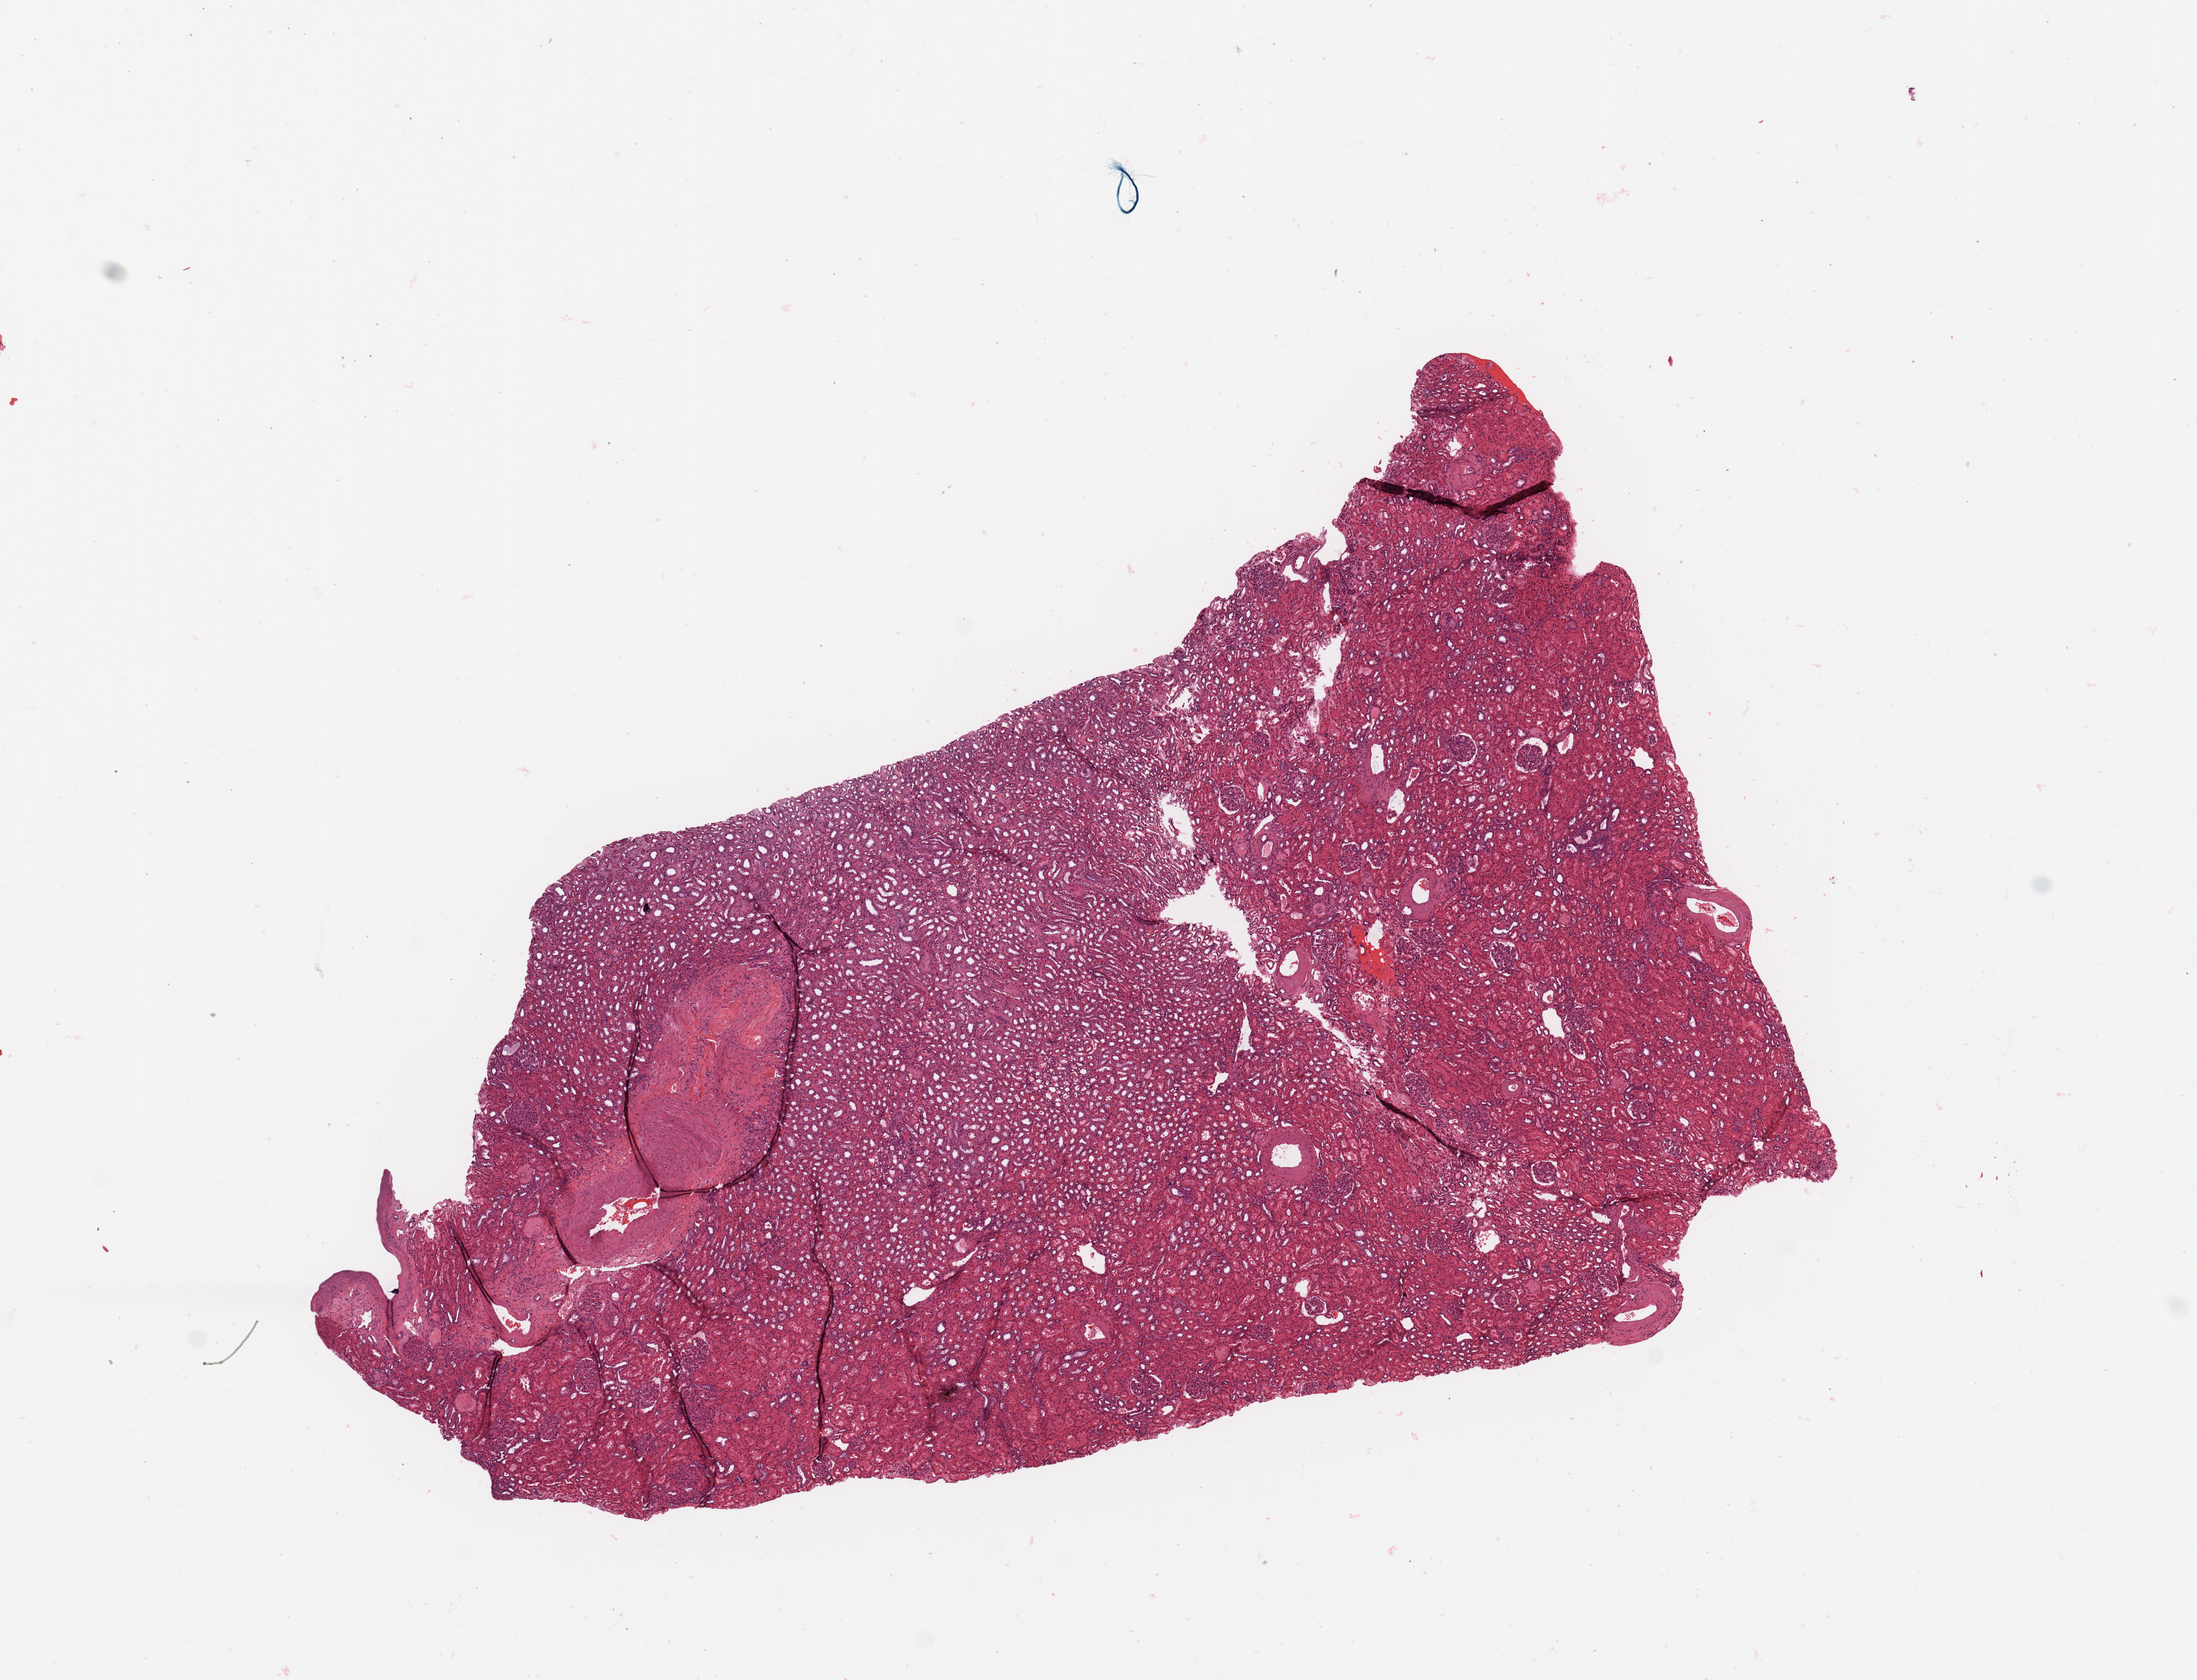
Digitized Hematoxylin and eosin (H&E) stained tissue section (whole slide), whole scanned area (about 11.8 x 9.0 mm, acquisition: 20x scan) shown as a low-resolution overview. Normal (non-tumour) tissue sample, sampled site: kidney. Female, 64 y/o.
This section: normal (non-tumour) tissue from the same patient. Patient diagnosis: Renal cell carcinoma, NOS.